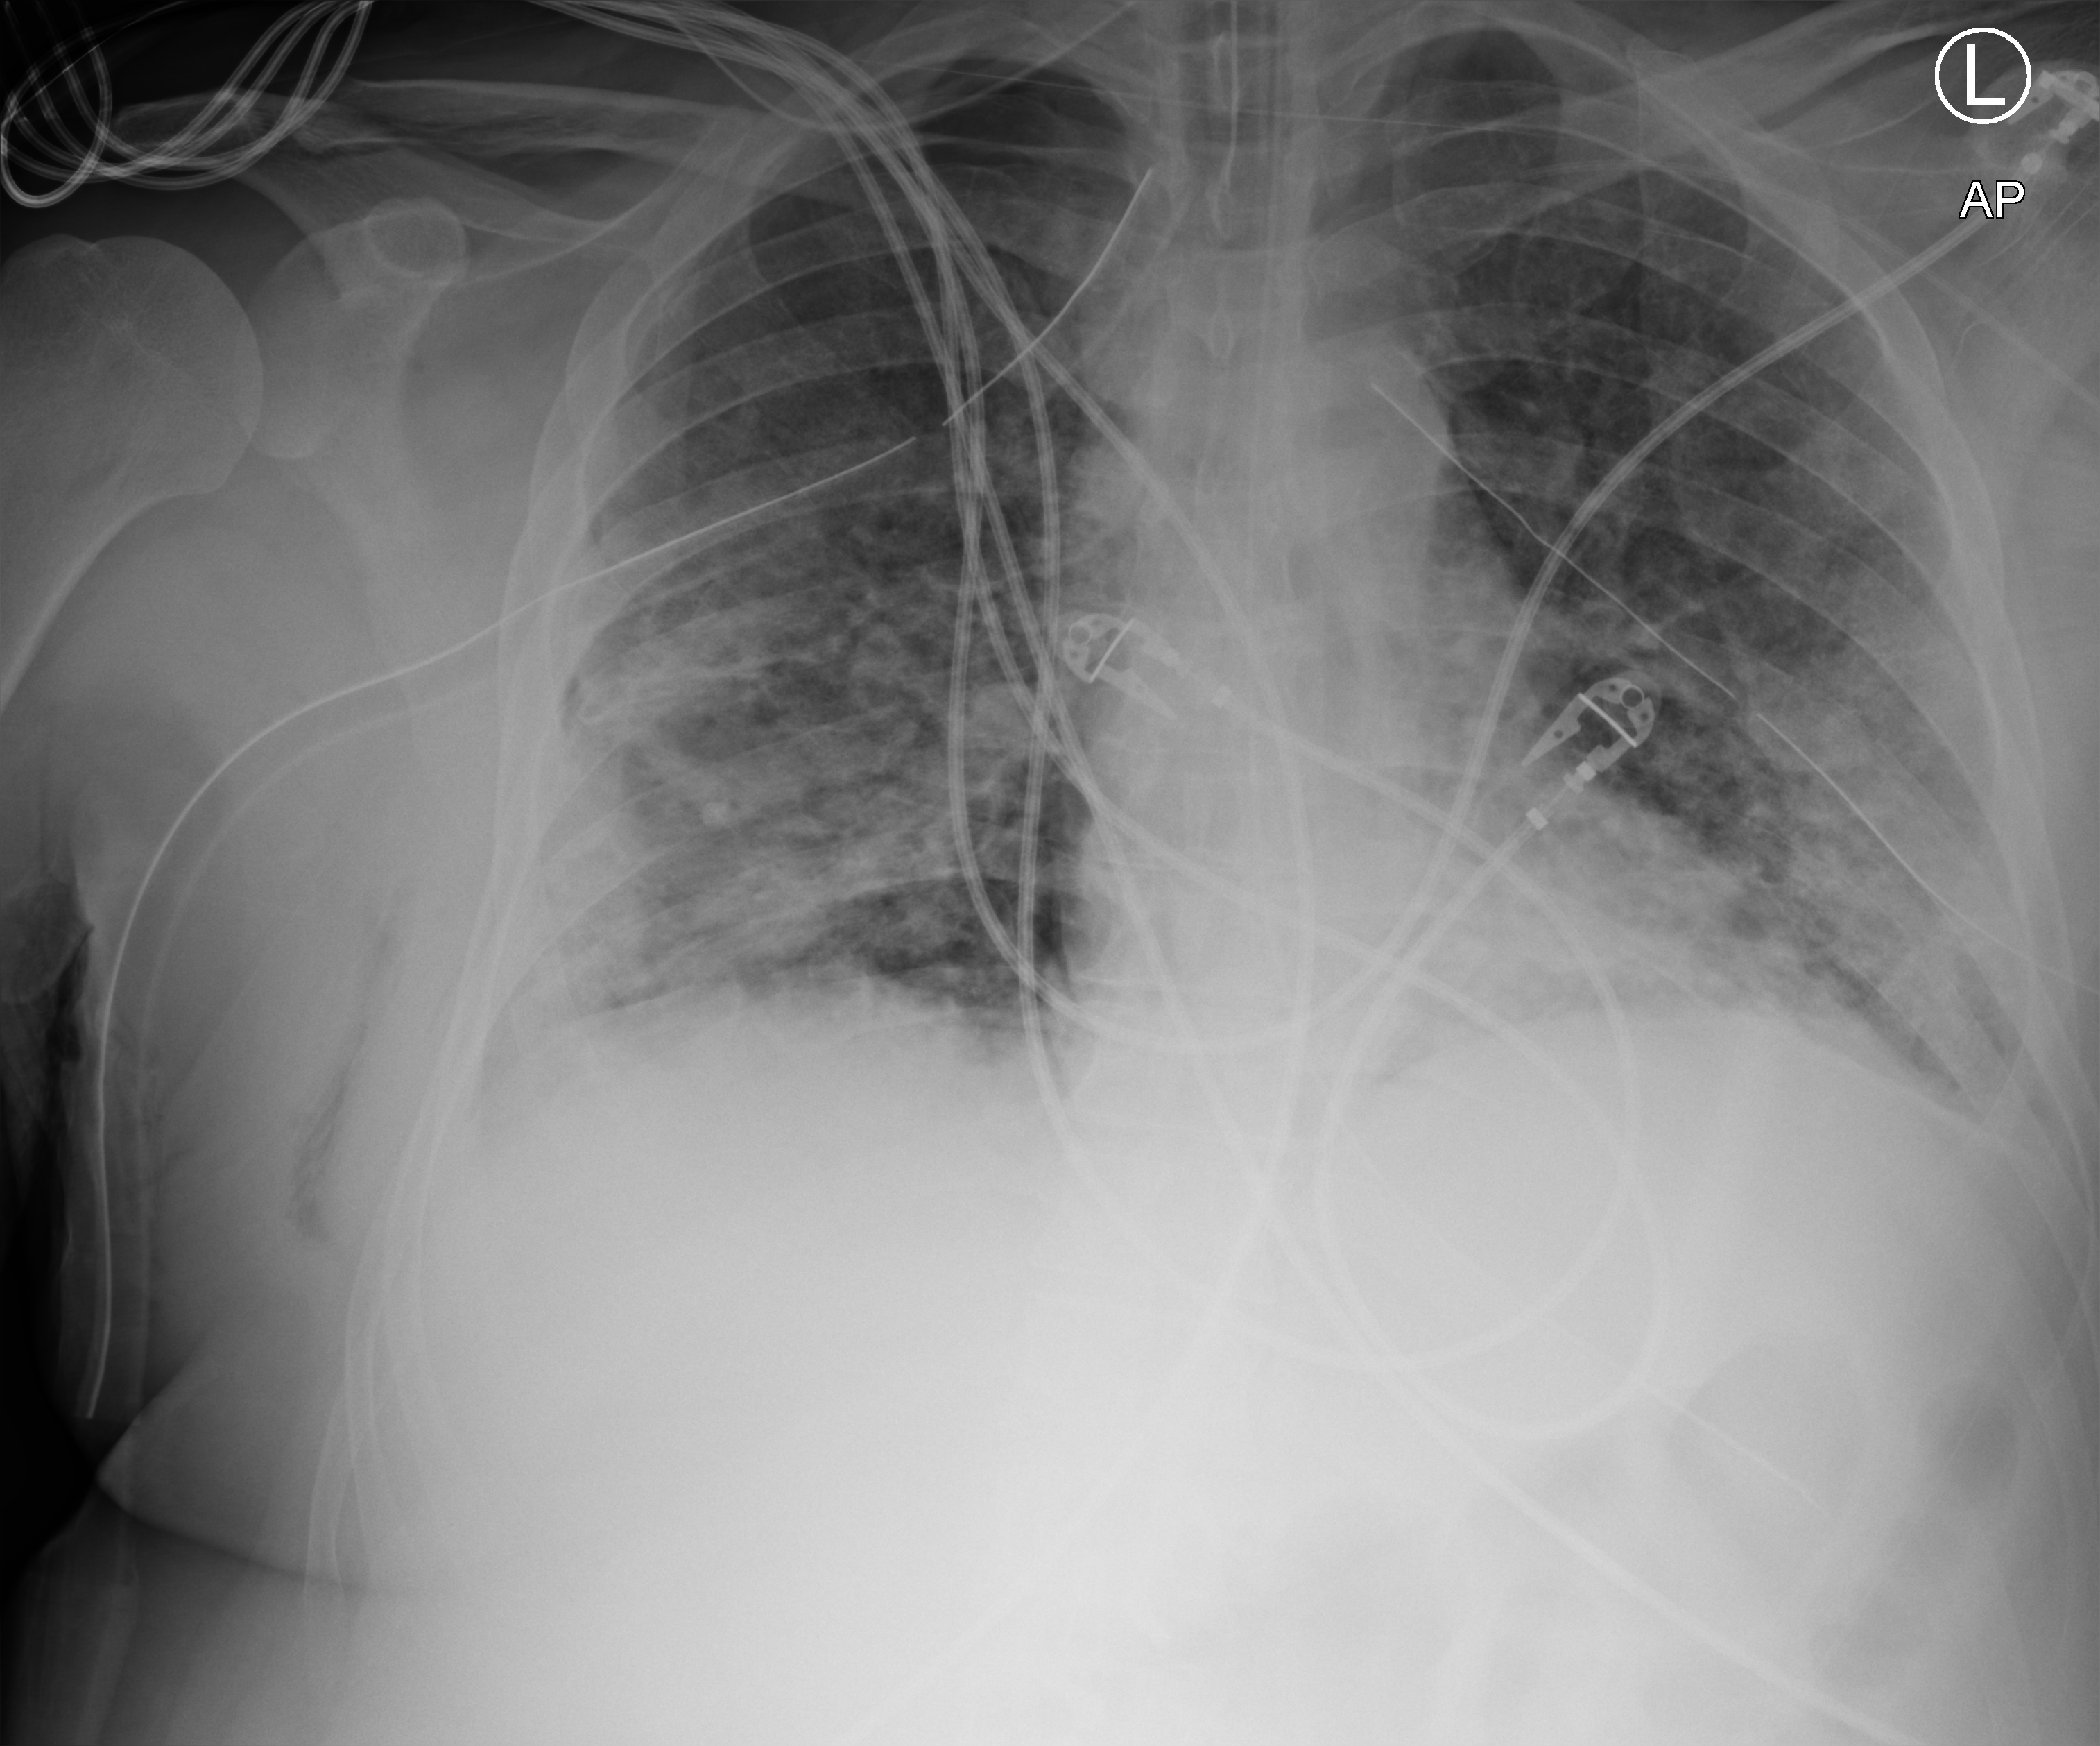
Chest X-ray (portable), anteroposterior (AP) projection. Male patient hospitalised with COVID-19, age 18–59 years.
Admission-level facts for this patient (not findings on this image; timing relative to this image not recorded): admitted to intensive care during this hospital stay: yes.